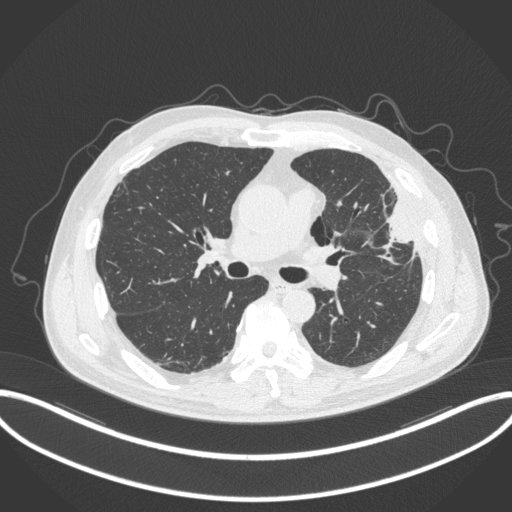
Chest CT, one axial slice; slice 196 of 382 in the series (ordered by position); reconstruction kernel B31f; 120 kVp; lung window (W 1500 / L -600 HU); 1 mm slice thickness; 512 × 512 image matrix, field of view 415 × 415 mm. Male patient, age 64 years. From the clinical record (not read from this slice): clinical TNM (as recorded): T4 N1 M0; histopathological grade: G3.
Outlined on this slice (rectangle marked by the reading radiologist):
- lung tumour (recorded histology: adenocarcinoma): bounding box <380,199,412,258> (left, top, right, bottom; pixels)